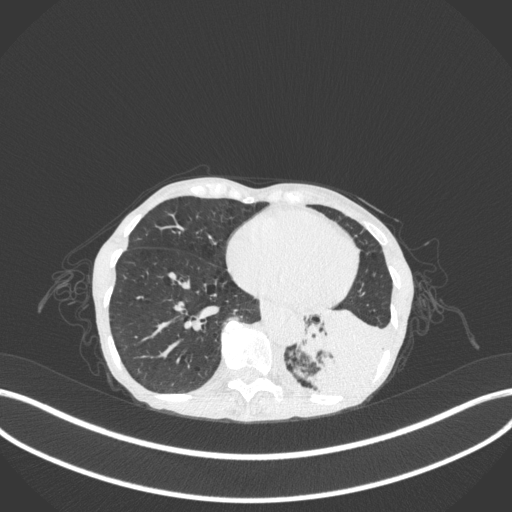
Chest CT, one axial slice. Slice 75 of 347 in the series (ordered by position). Reconstruction kernel B31f. 120 kVp. Lung window (W 1500 / L -600 HU). 1 mm slice thickness. 512 × 512 image matrix, field of view 400 × 400 mm. Patient: female, 70 years. From the clinical record (not read from this slice): clinical TNM (as recorded): T3 N0 M0; histopathological grade: G3.
Structures marked on this image (bounding box drawn by a radiologist):
- lung tumour (recorded histology: small cell carcinoma): bounding box [x1, y1, x2, y2] px = [298, 295, 394, 403]